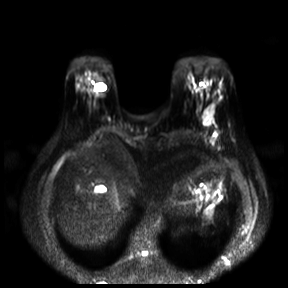
Breast MRI, one axial slice. Slice 4 of 30 in the series (ordered by position). Diffusion-weighted series; image 2 of 4 stored at this slice position (different b-values; order by instance number). 3 T. 4 mm slice thickness. 288 × 288 image matrix, field of view 360 × 360 mm. Female patient.
Outlined on this slice (manually delineated by an expert):
- tumour on diffusion-weighted imaging: box from (x=203, y=105) to (x=214, y=124) px